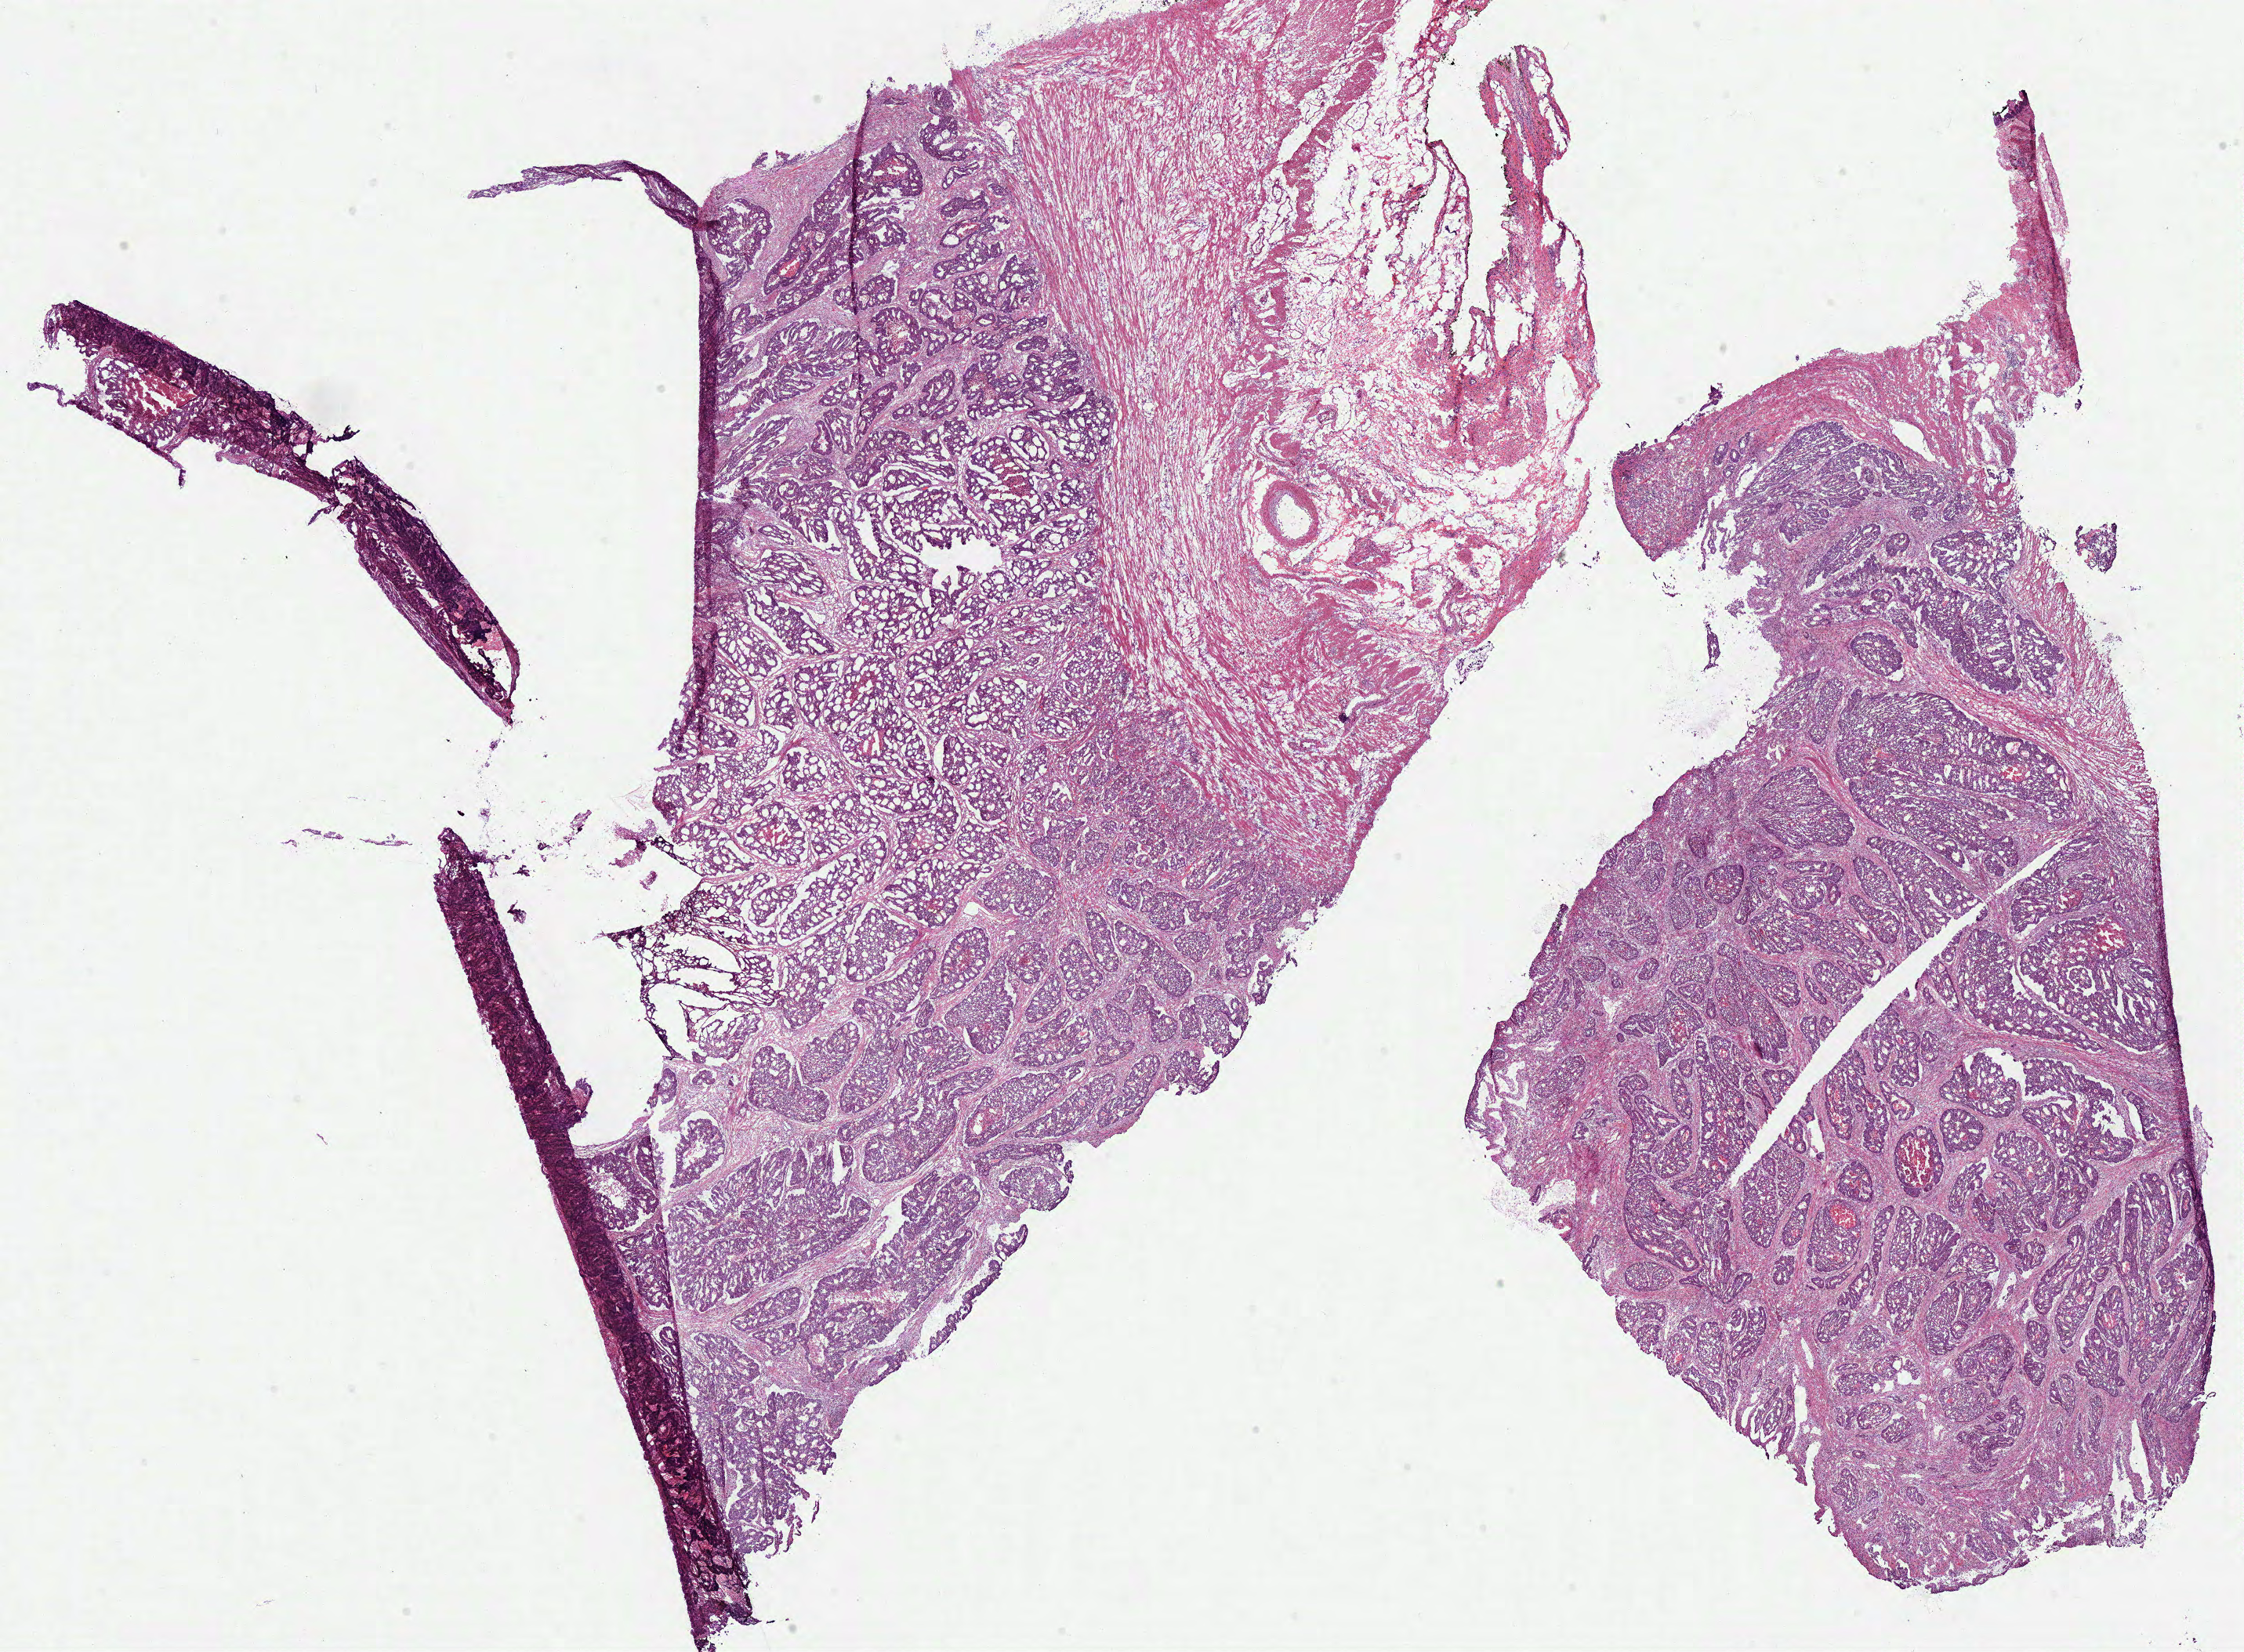
Digitized Hematoxylin and eosin (H&E) stained tissue section (whole slide) — low-resolution overview of the scanned area, about 22.5 x 16.6 mm. Frozen section. Sample: primary tumour, colon. Female, age 48 years at initial diagnosis. Composition of this section per pathologist review: tumour cells 67%, tumour nuclei 80%, normal cells 5%, stromal cells 20%, necrosis 8%.
AJCC pathologic stage: I. TNM: T2 N0 M0. Diagnosis: Adenocarcinoma, NOS (ascending colon).